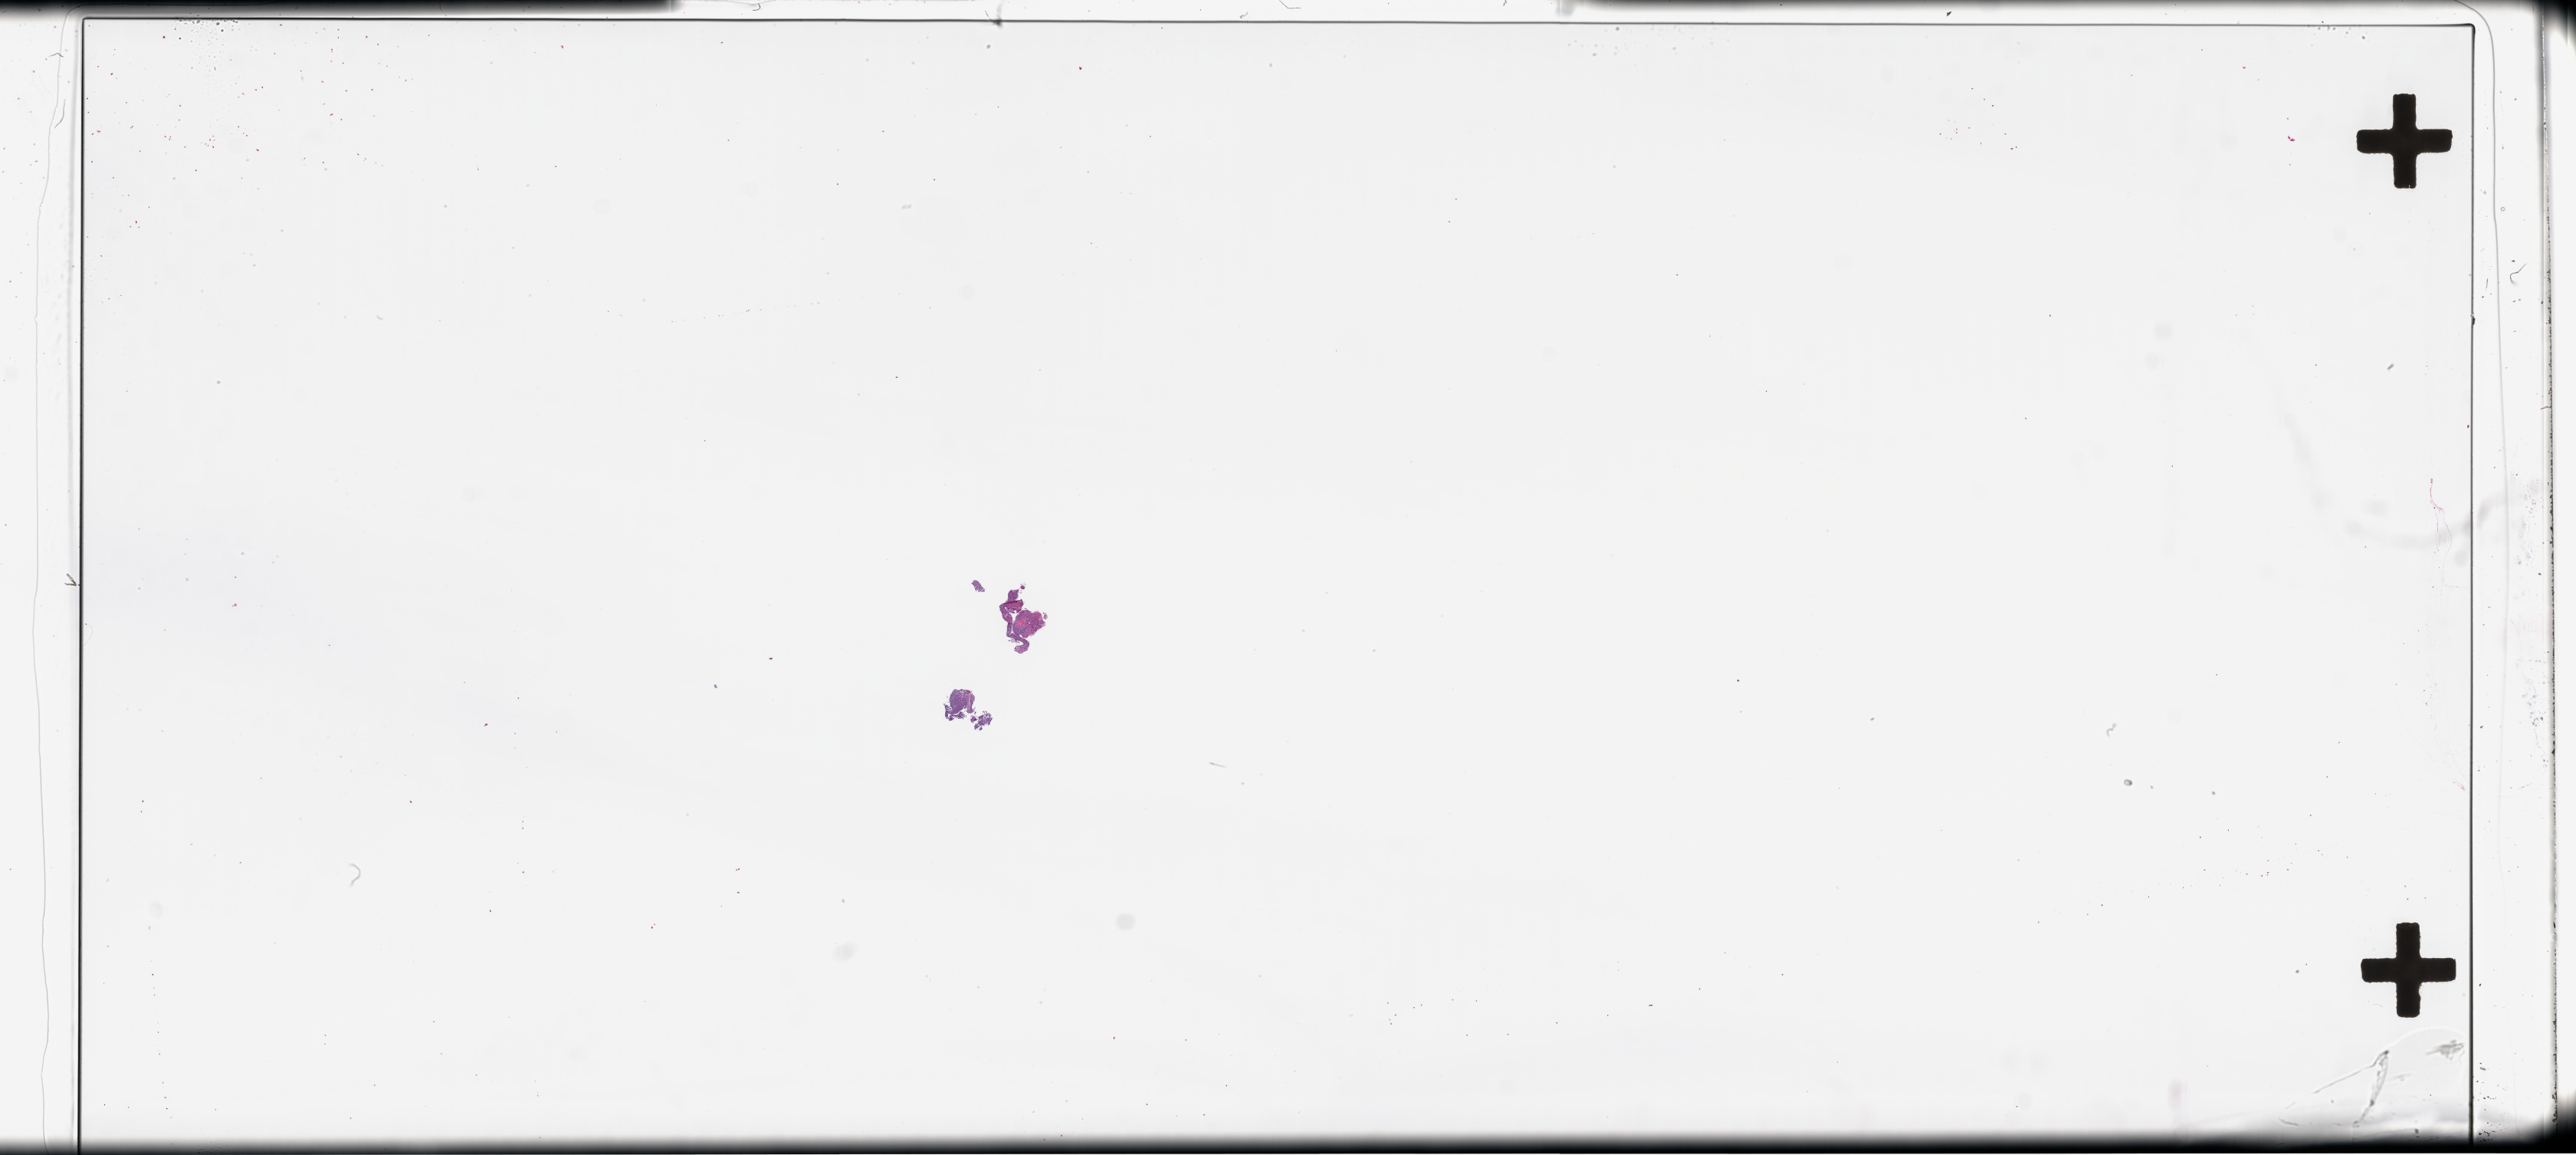
Digitized haematoxylin and eosin-stained section, shown as a low-resolution overview of the whole scanned area (about 54.3 x 24.3 mm); FFPE section; specimen time point: collected at baseline (before treatment). Male patient.
This section: metastatic tumor tissue. Patient diagnosis (primary): Melanoma.